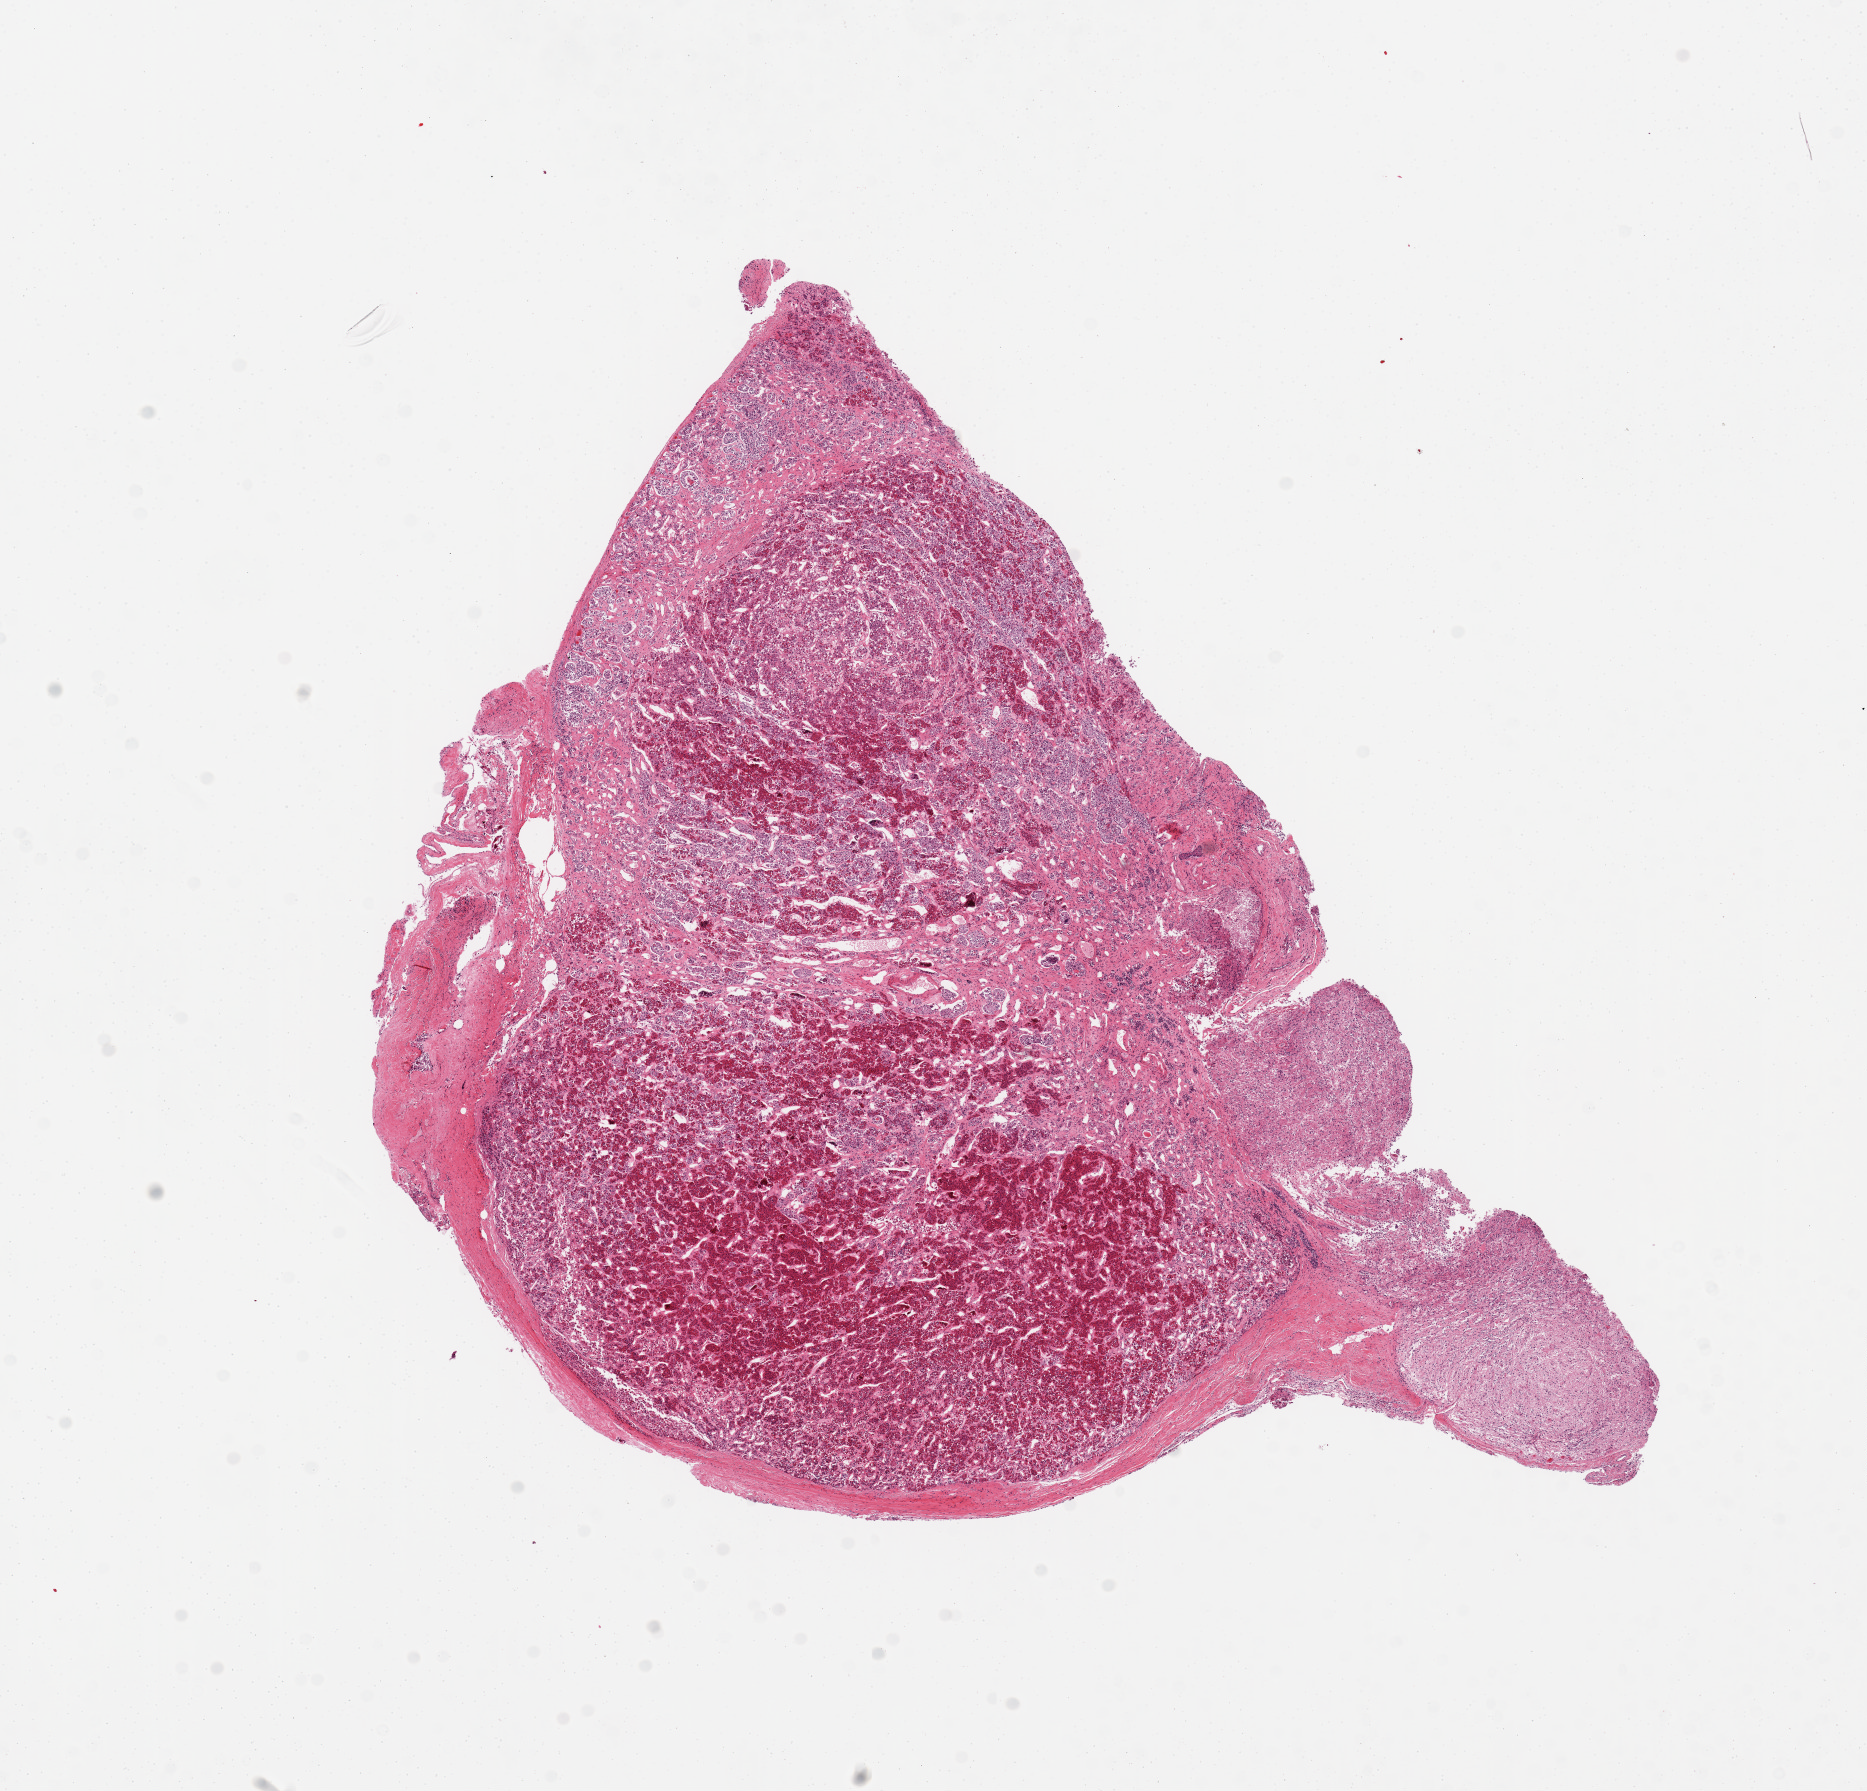
Haematoxylin and eosin whole-slide image, shown as a low-resolution overview of the whole scanned area (about 14.8 x 14.2 mm); PAXgene-fixed paraffin-embedded (PFPE) section; target tissue: pituitary; tissue donor sample. Donor sex: female.
Pathologist's review note for this sample: 1 piece, mainly adenohypophysis; ~5x2.5mm portion of neurohypophysis present, but all badly autolyzed.